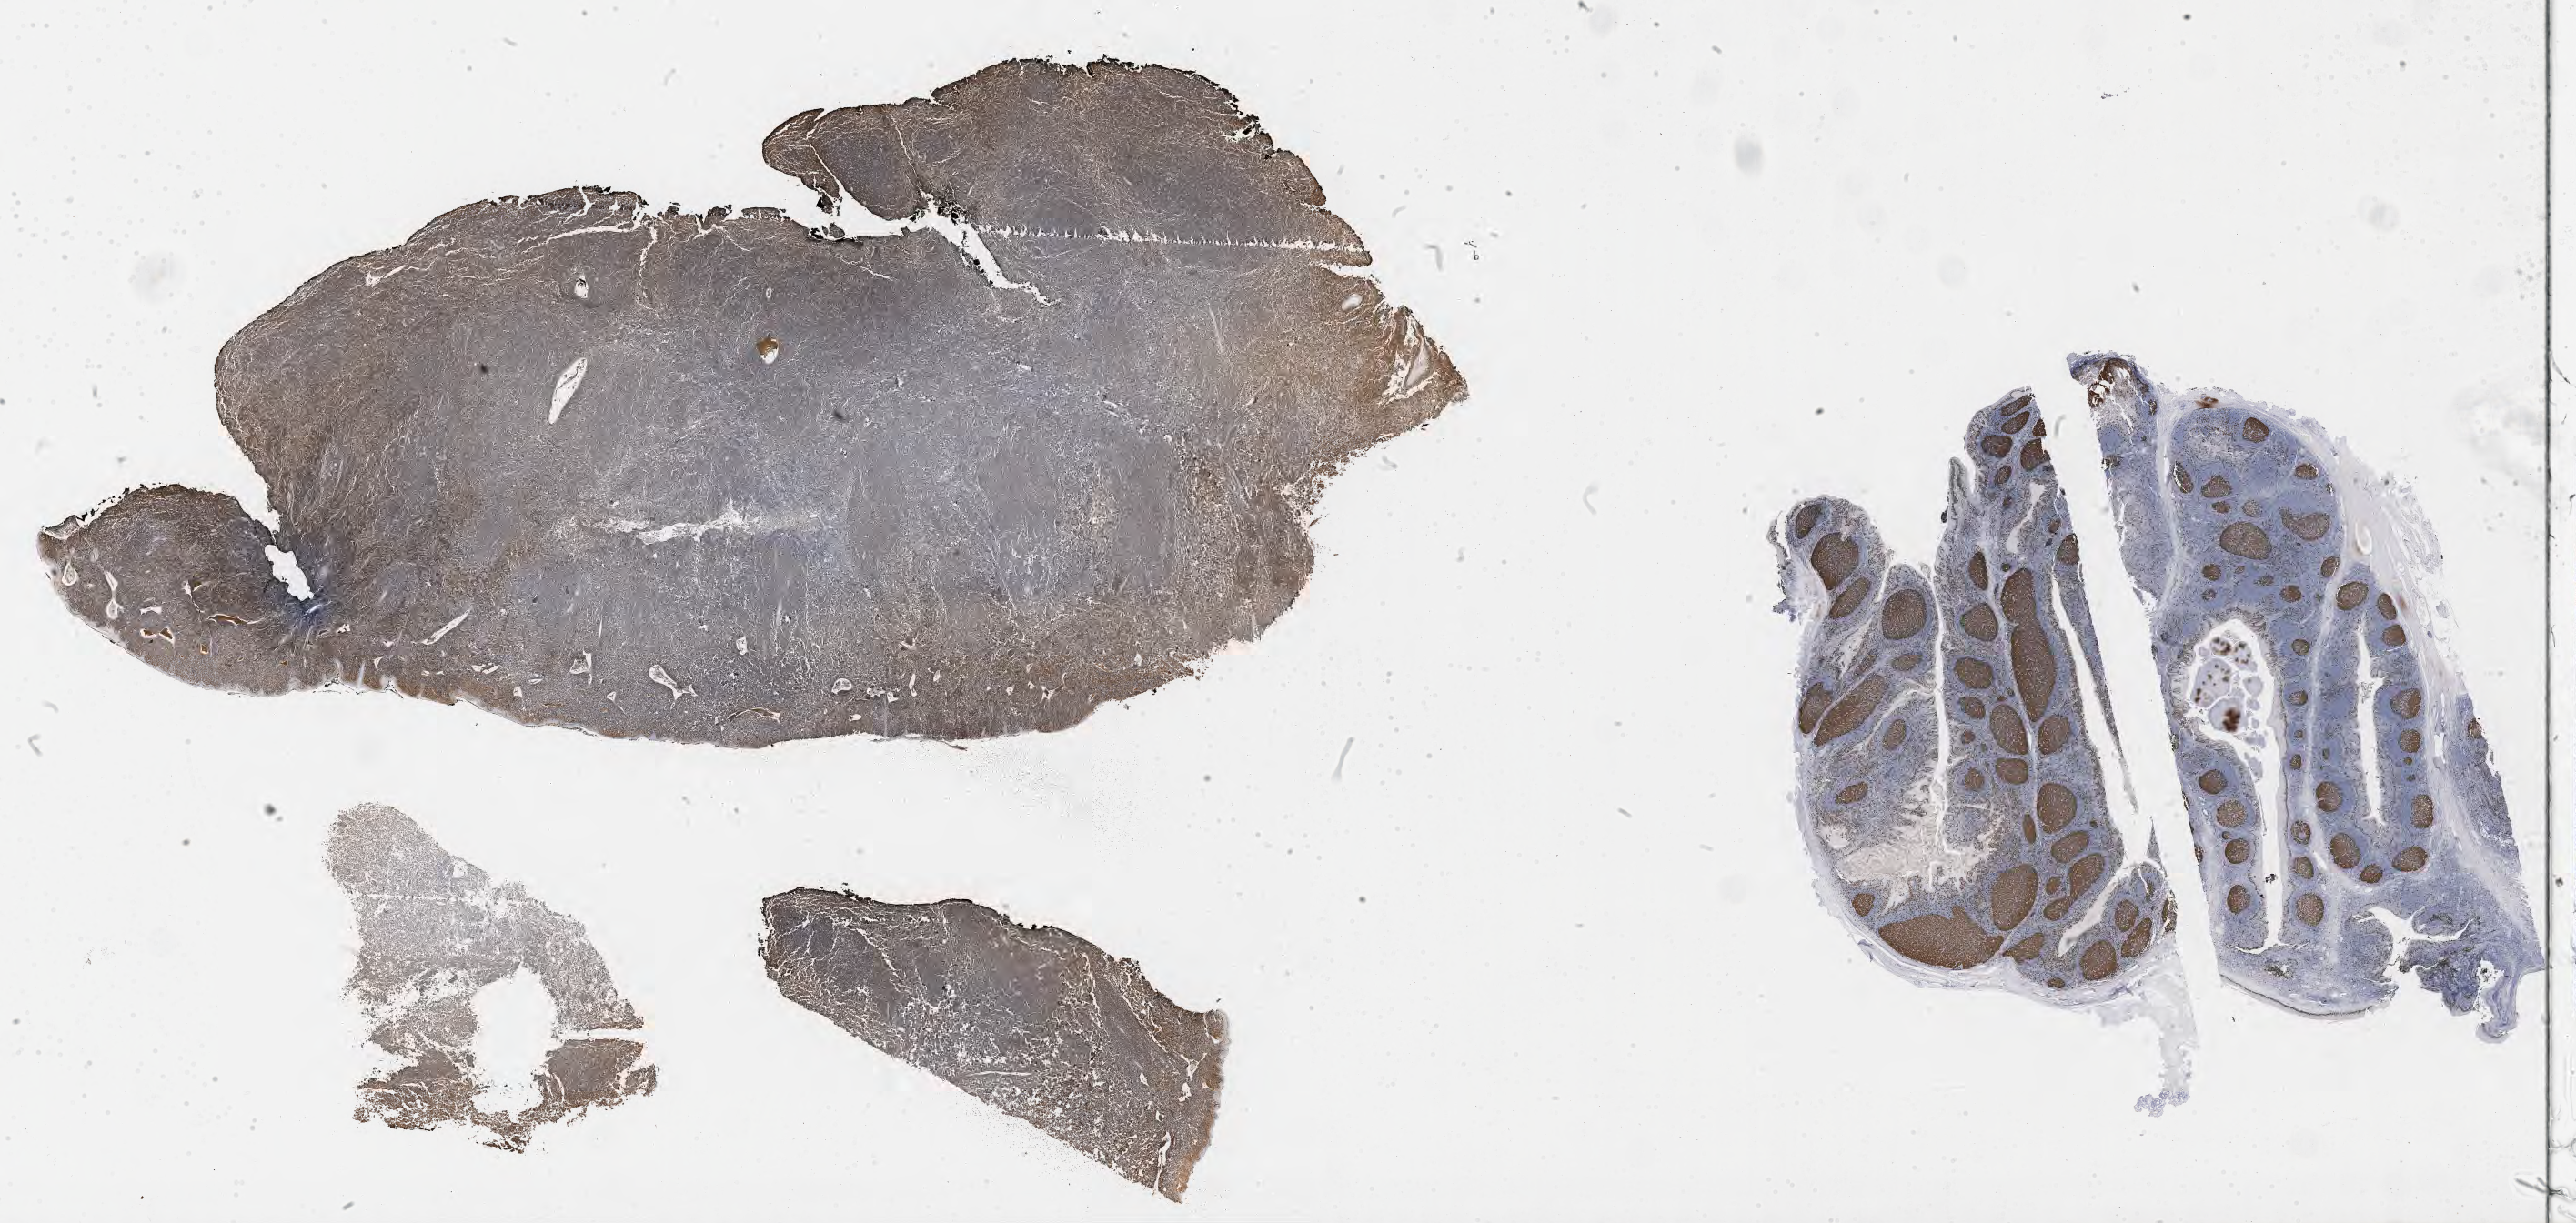
Whole-slide image, immunohistochemical stain for Ki-67 — whole scanned area (about 45.8 x 21.7 mm) shown as a low-resolution overview; specimen: tumor tissue. Patient male; age 46 years.
* diagnosis: Burkitt lymphoma, NOS